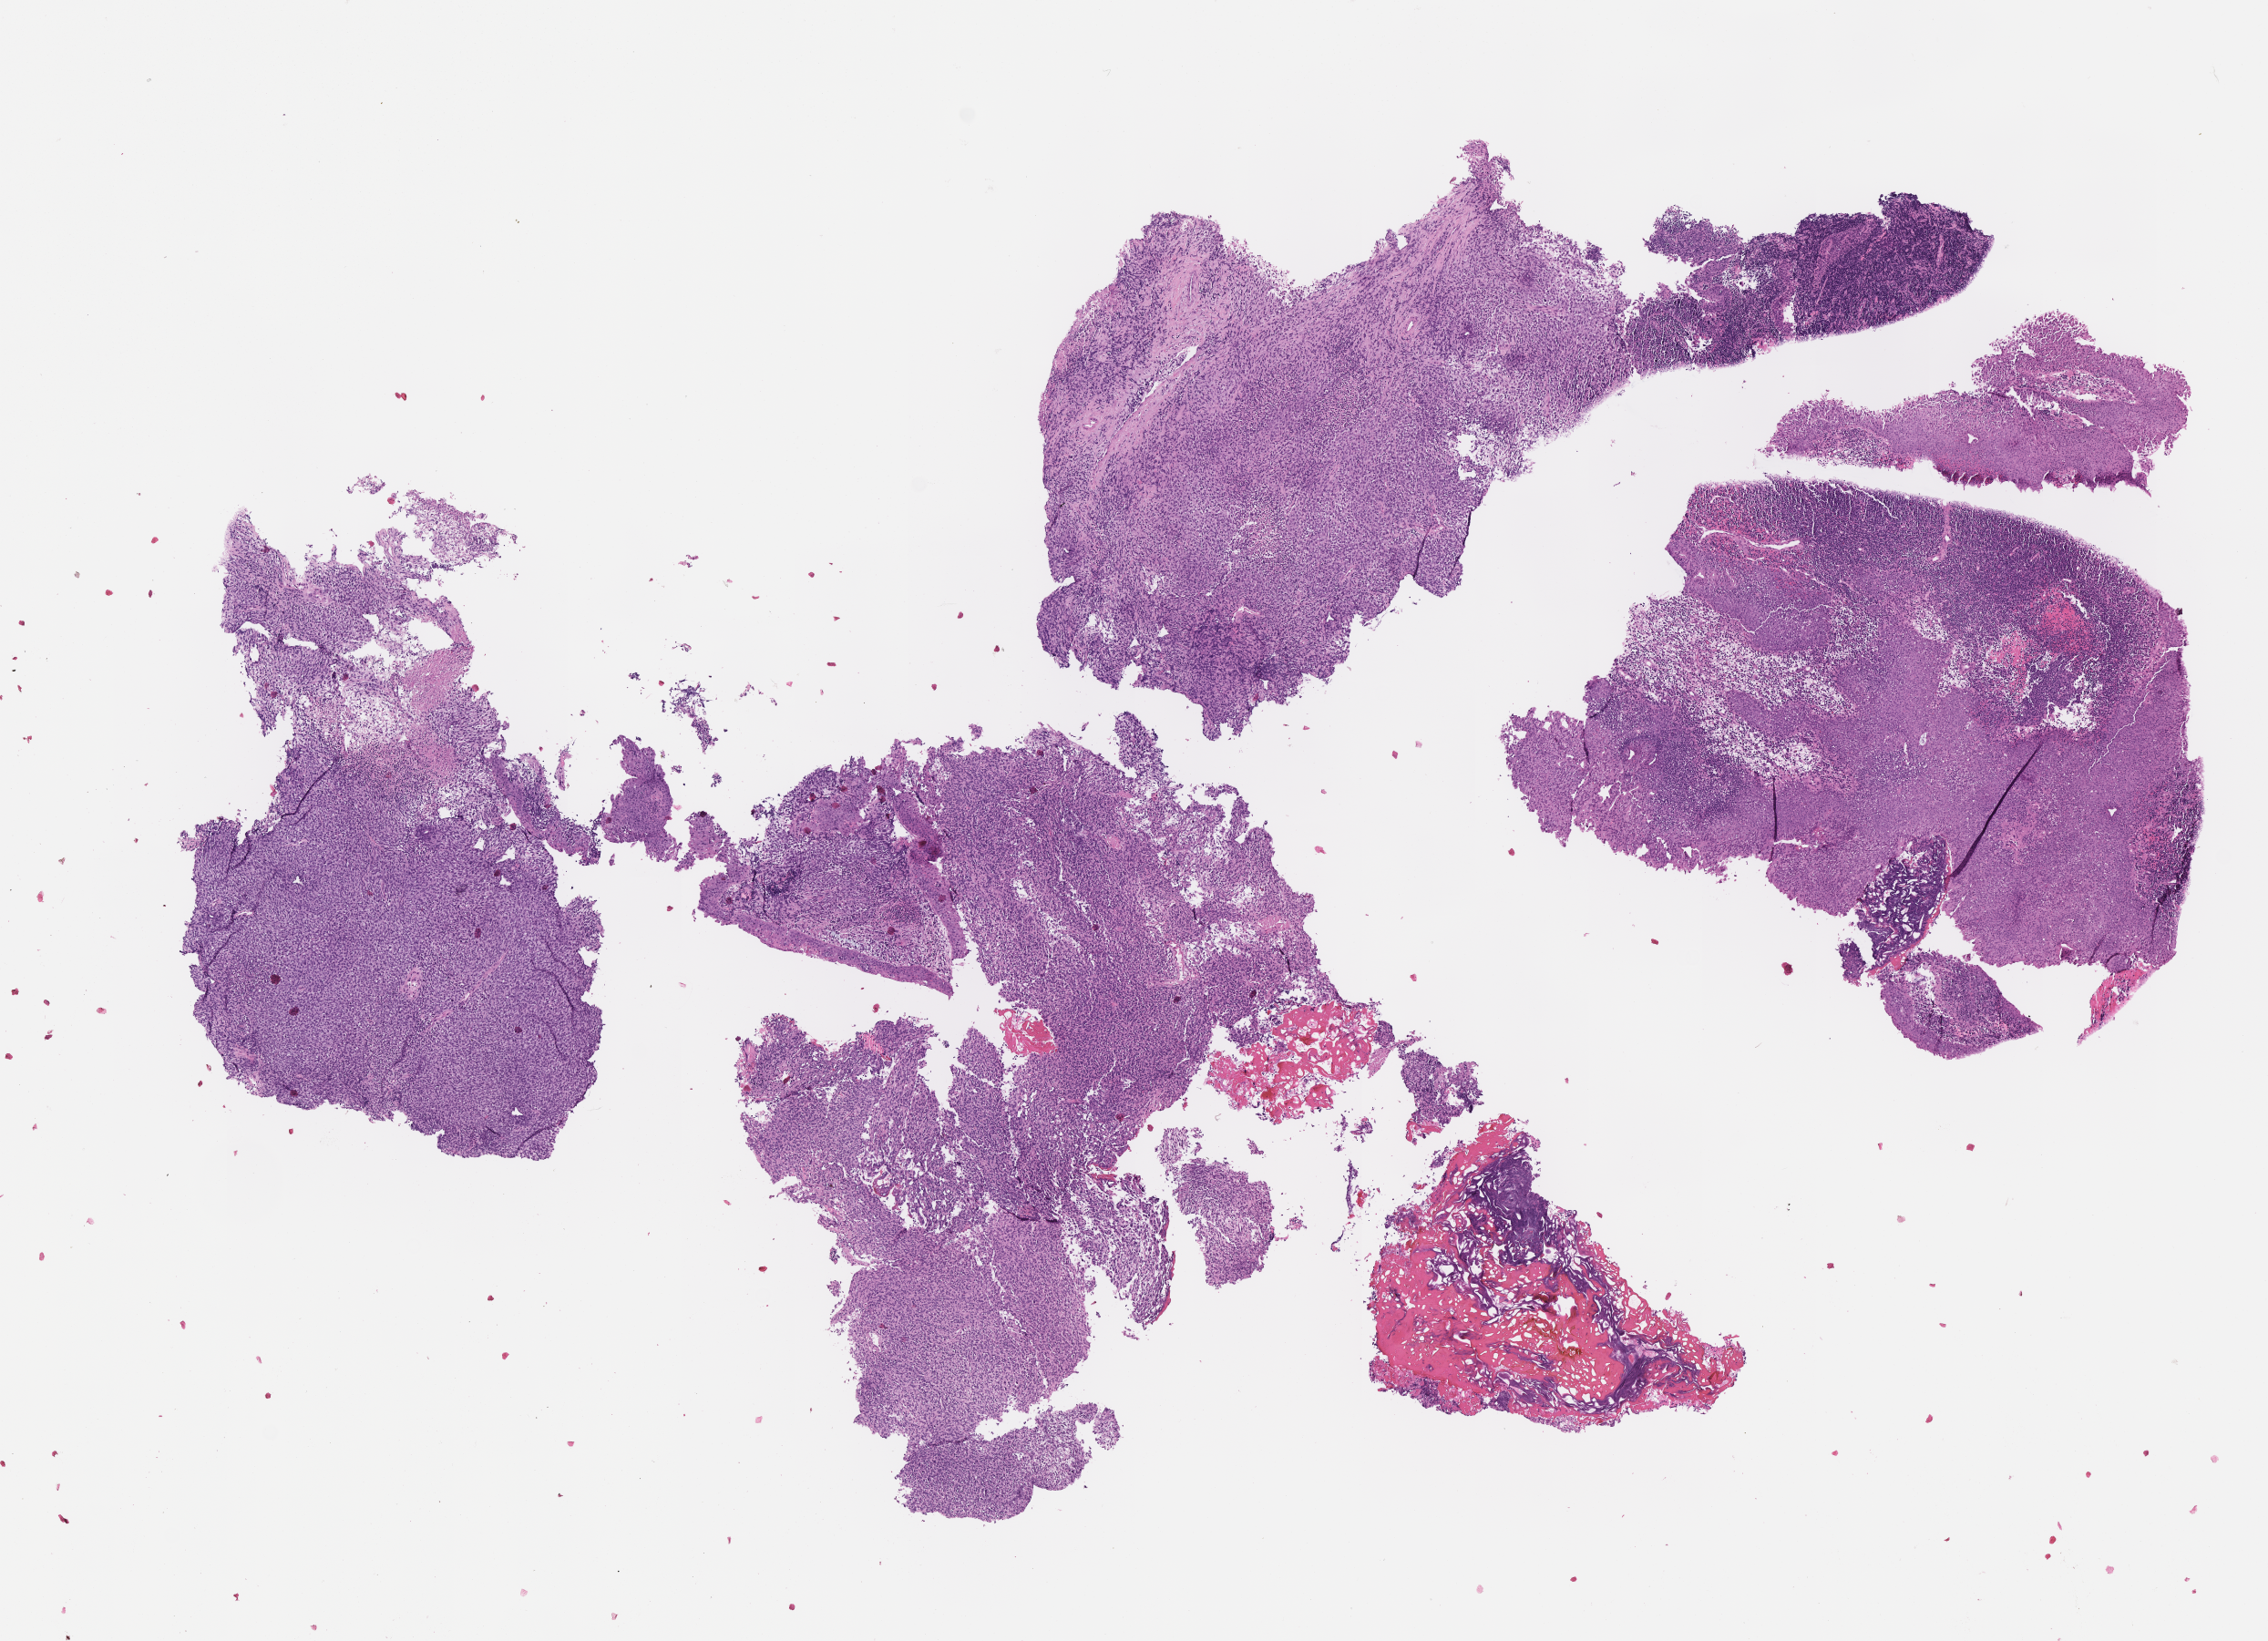
Digitized hematoxylin and eosin (H&E)-stained section of tumor tissue — a low-resolution overview of the entire scanned area, about 10.1 x 7.3 mm. Formalin-fixed, paraffin-embedded (FFPE) tissue. Sample anatomic site: nasopharynx. Patient: male, age 4.9 years at diagnosis.
Primary site (case record): parapharyngeal Area. Stage (as recorded): 3. Metastatic status at presentation (as recorded): non-metastatic. Diagnosis: rhabdomyosarcoma; histological classification: embryonal rhabdomyosarcoma.